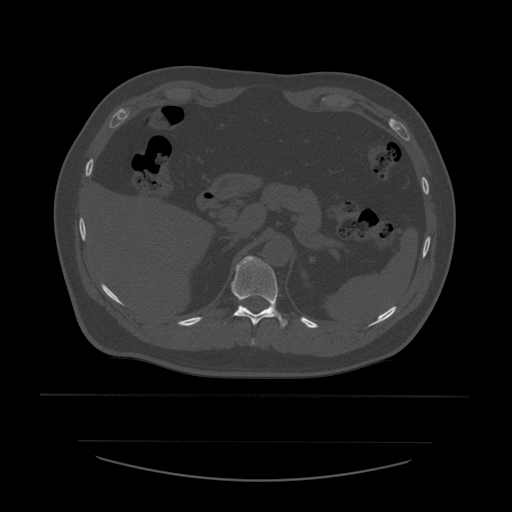
CT including the spine, one axial slice; slice 274 of 532 in the series (ordered by position); reconstruction kernel STANDARD; 120 kVp; bone window (W 1800 / L 400 HU); 1.25 mm slice thickness; 512 × 512 image matrix, field of view 441 × 441 mm. Patient age 44 years. Case-level facts recorded for this patient, not image findings: primary cancer: soft tissue sarcoma.
Outlined on this slice (semi-automatically segmented with operator editing):
- T10 vertebra: bounding box [x1, y1, x2, y2] px = [251, 338, 256, 345]
- T11 vertebra: [225, 256, 288, 329]